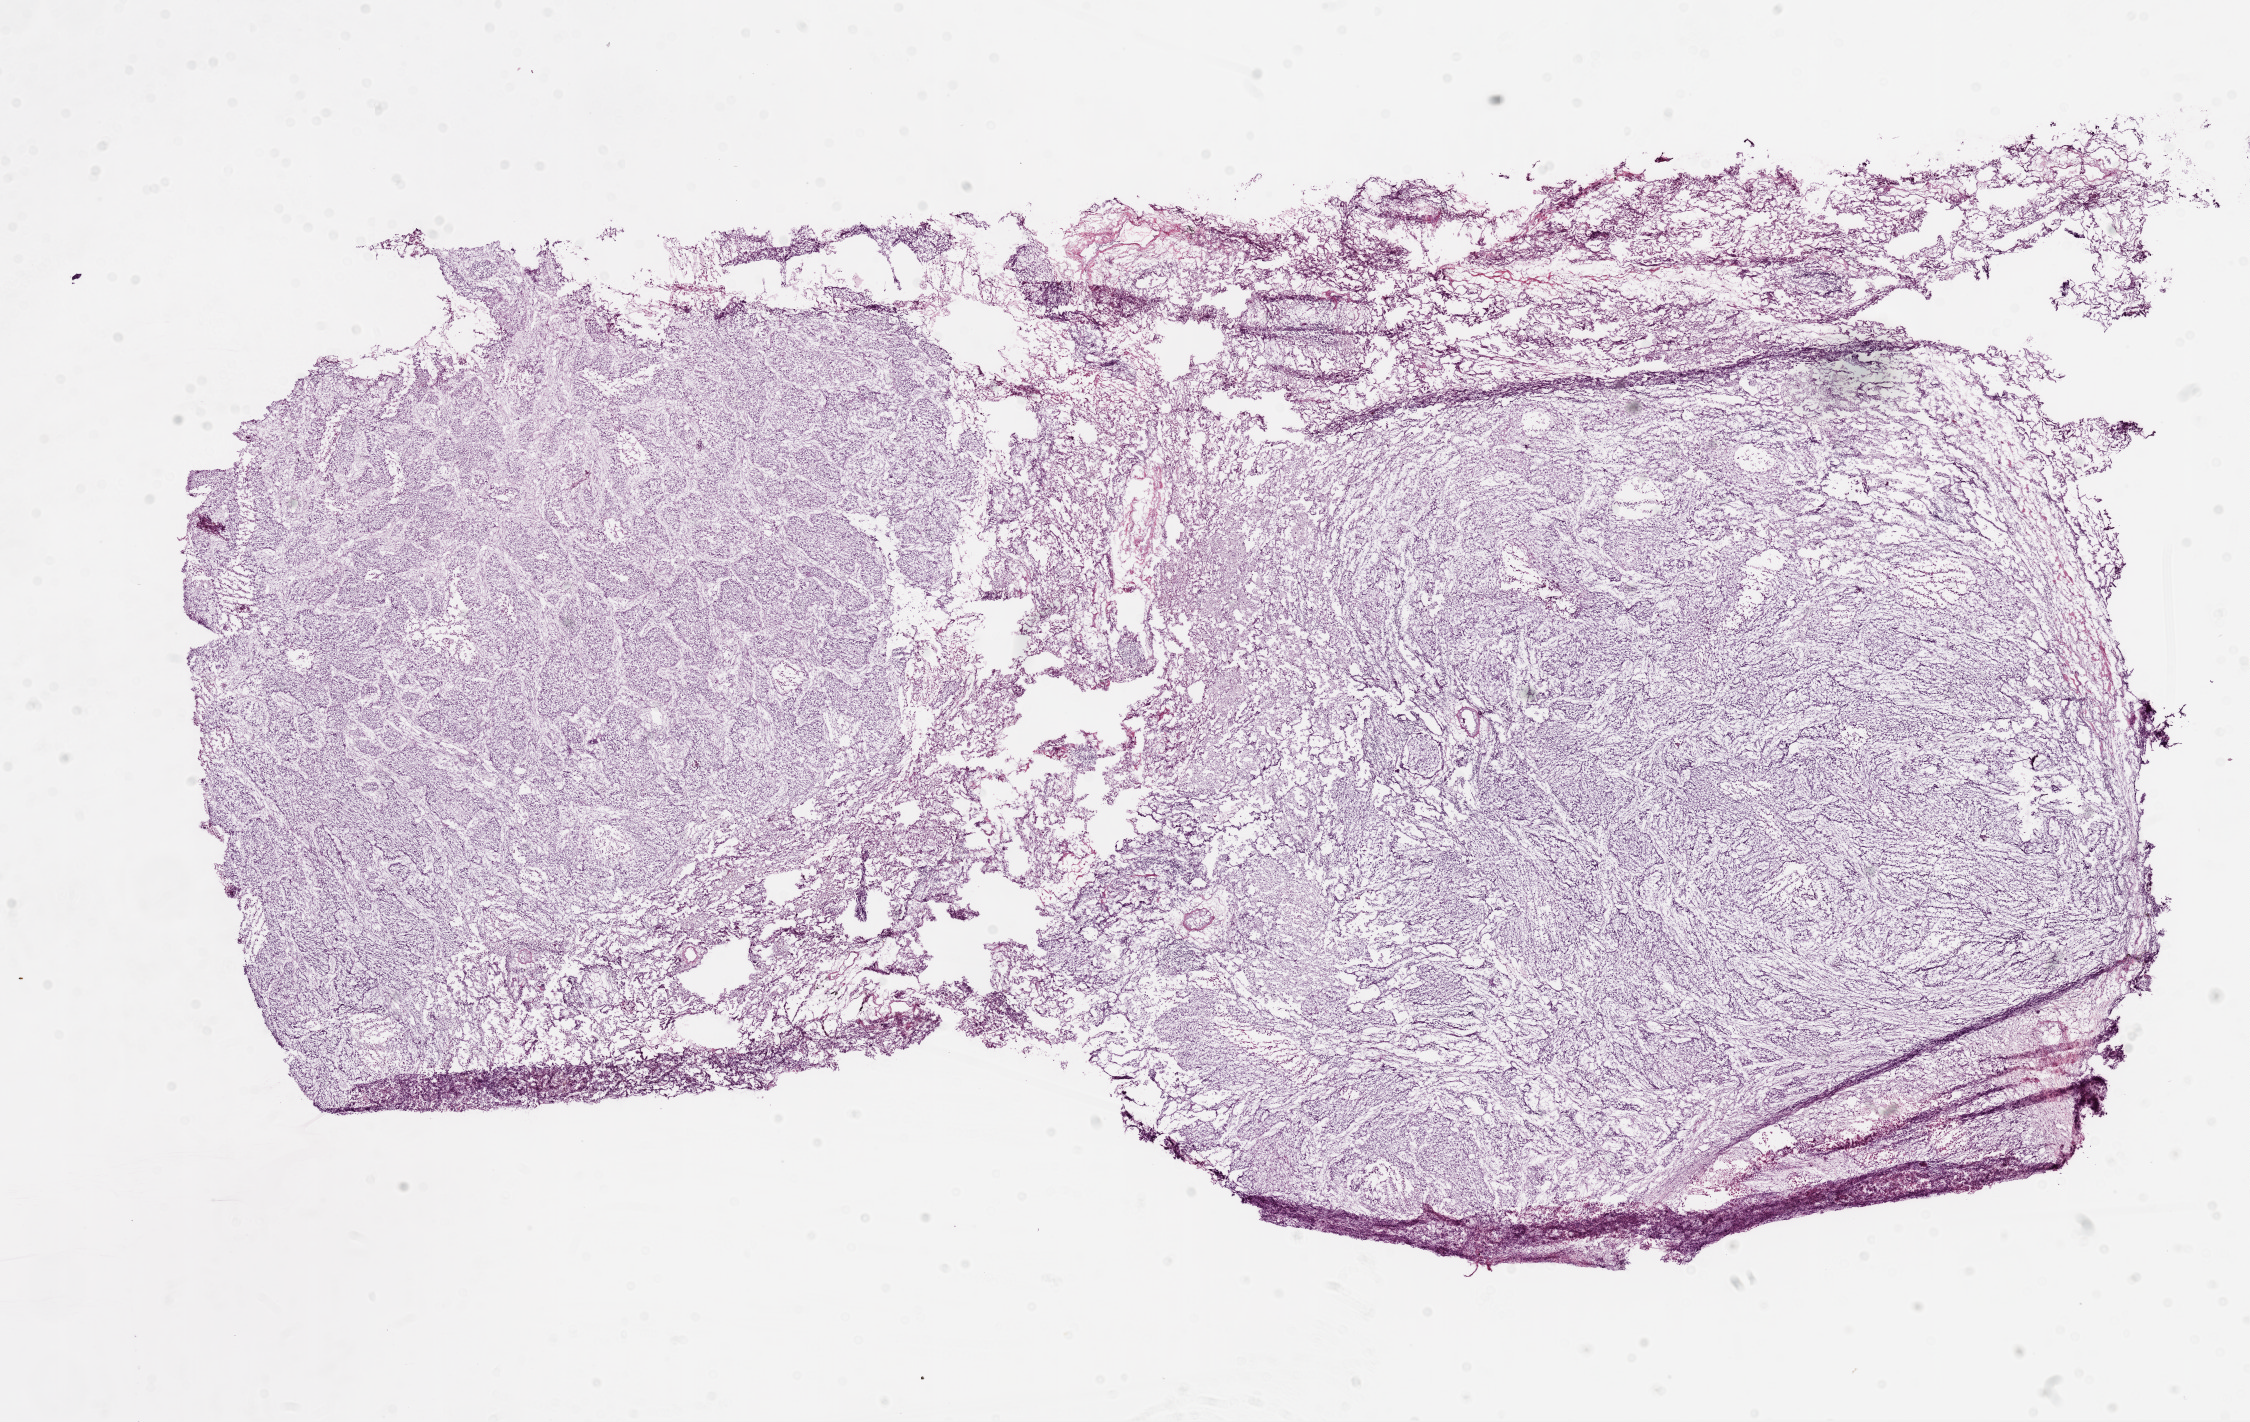
H&E whole-slide image — whole scanned area (about 18.1 x 11.4 mm, slide scanned at 20x) shown as a low-resolution overview, frozen section from the top of the tissue portion, sample: primary tumour, lung. Male patient; age at initial diagnosis 62 years.
Histologic diagnosis: Squamous cell carcinoma, NOS (lower lobe, lung).